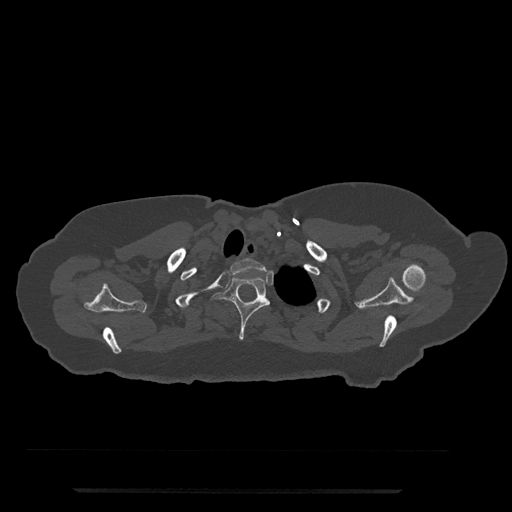
CT including the spine, one axial slice. Slice 677 of 797 in the series (ordered by position). Reconstruction kernel Br40s/3. Bone window (W 1800 / L 400 HU). 0.5 mm slice thickness. 512 × 512 image matrix. Patient: female, 51 years. Case-level facts recorded for this patient, not image findings: primary cancer: neuro; vertebrae with lytic lesions (as recorded): T8.
Structures marked on this image (semi-automatic segmentation, software-assisted and operator-edited):
- T1 vertebra: bounding box [x1, y1, x2, y2] px = [230, 258, 267, 274]
- T2 vertebra: [212, 275, 270, 341]